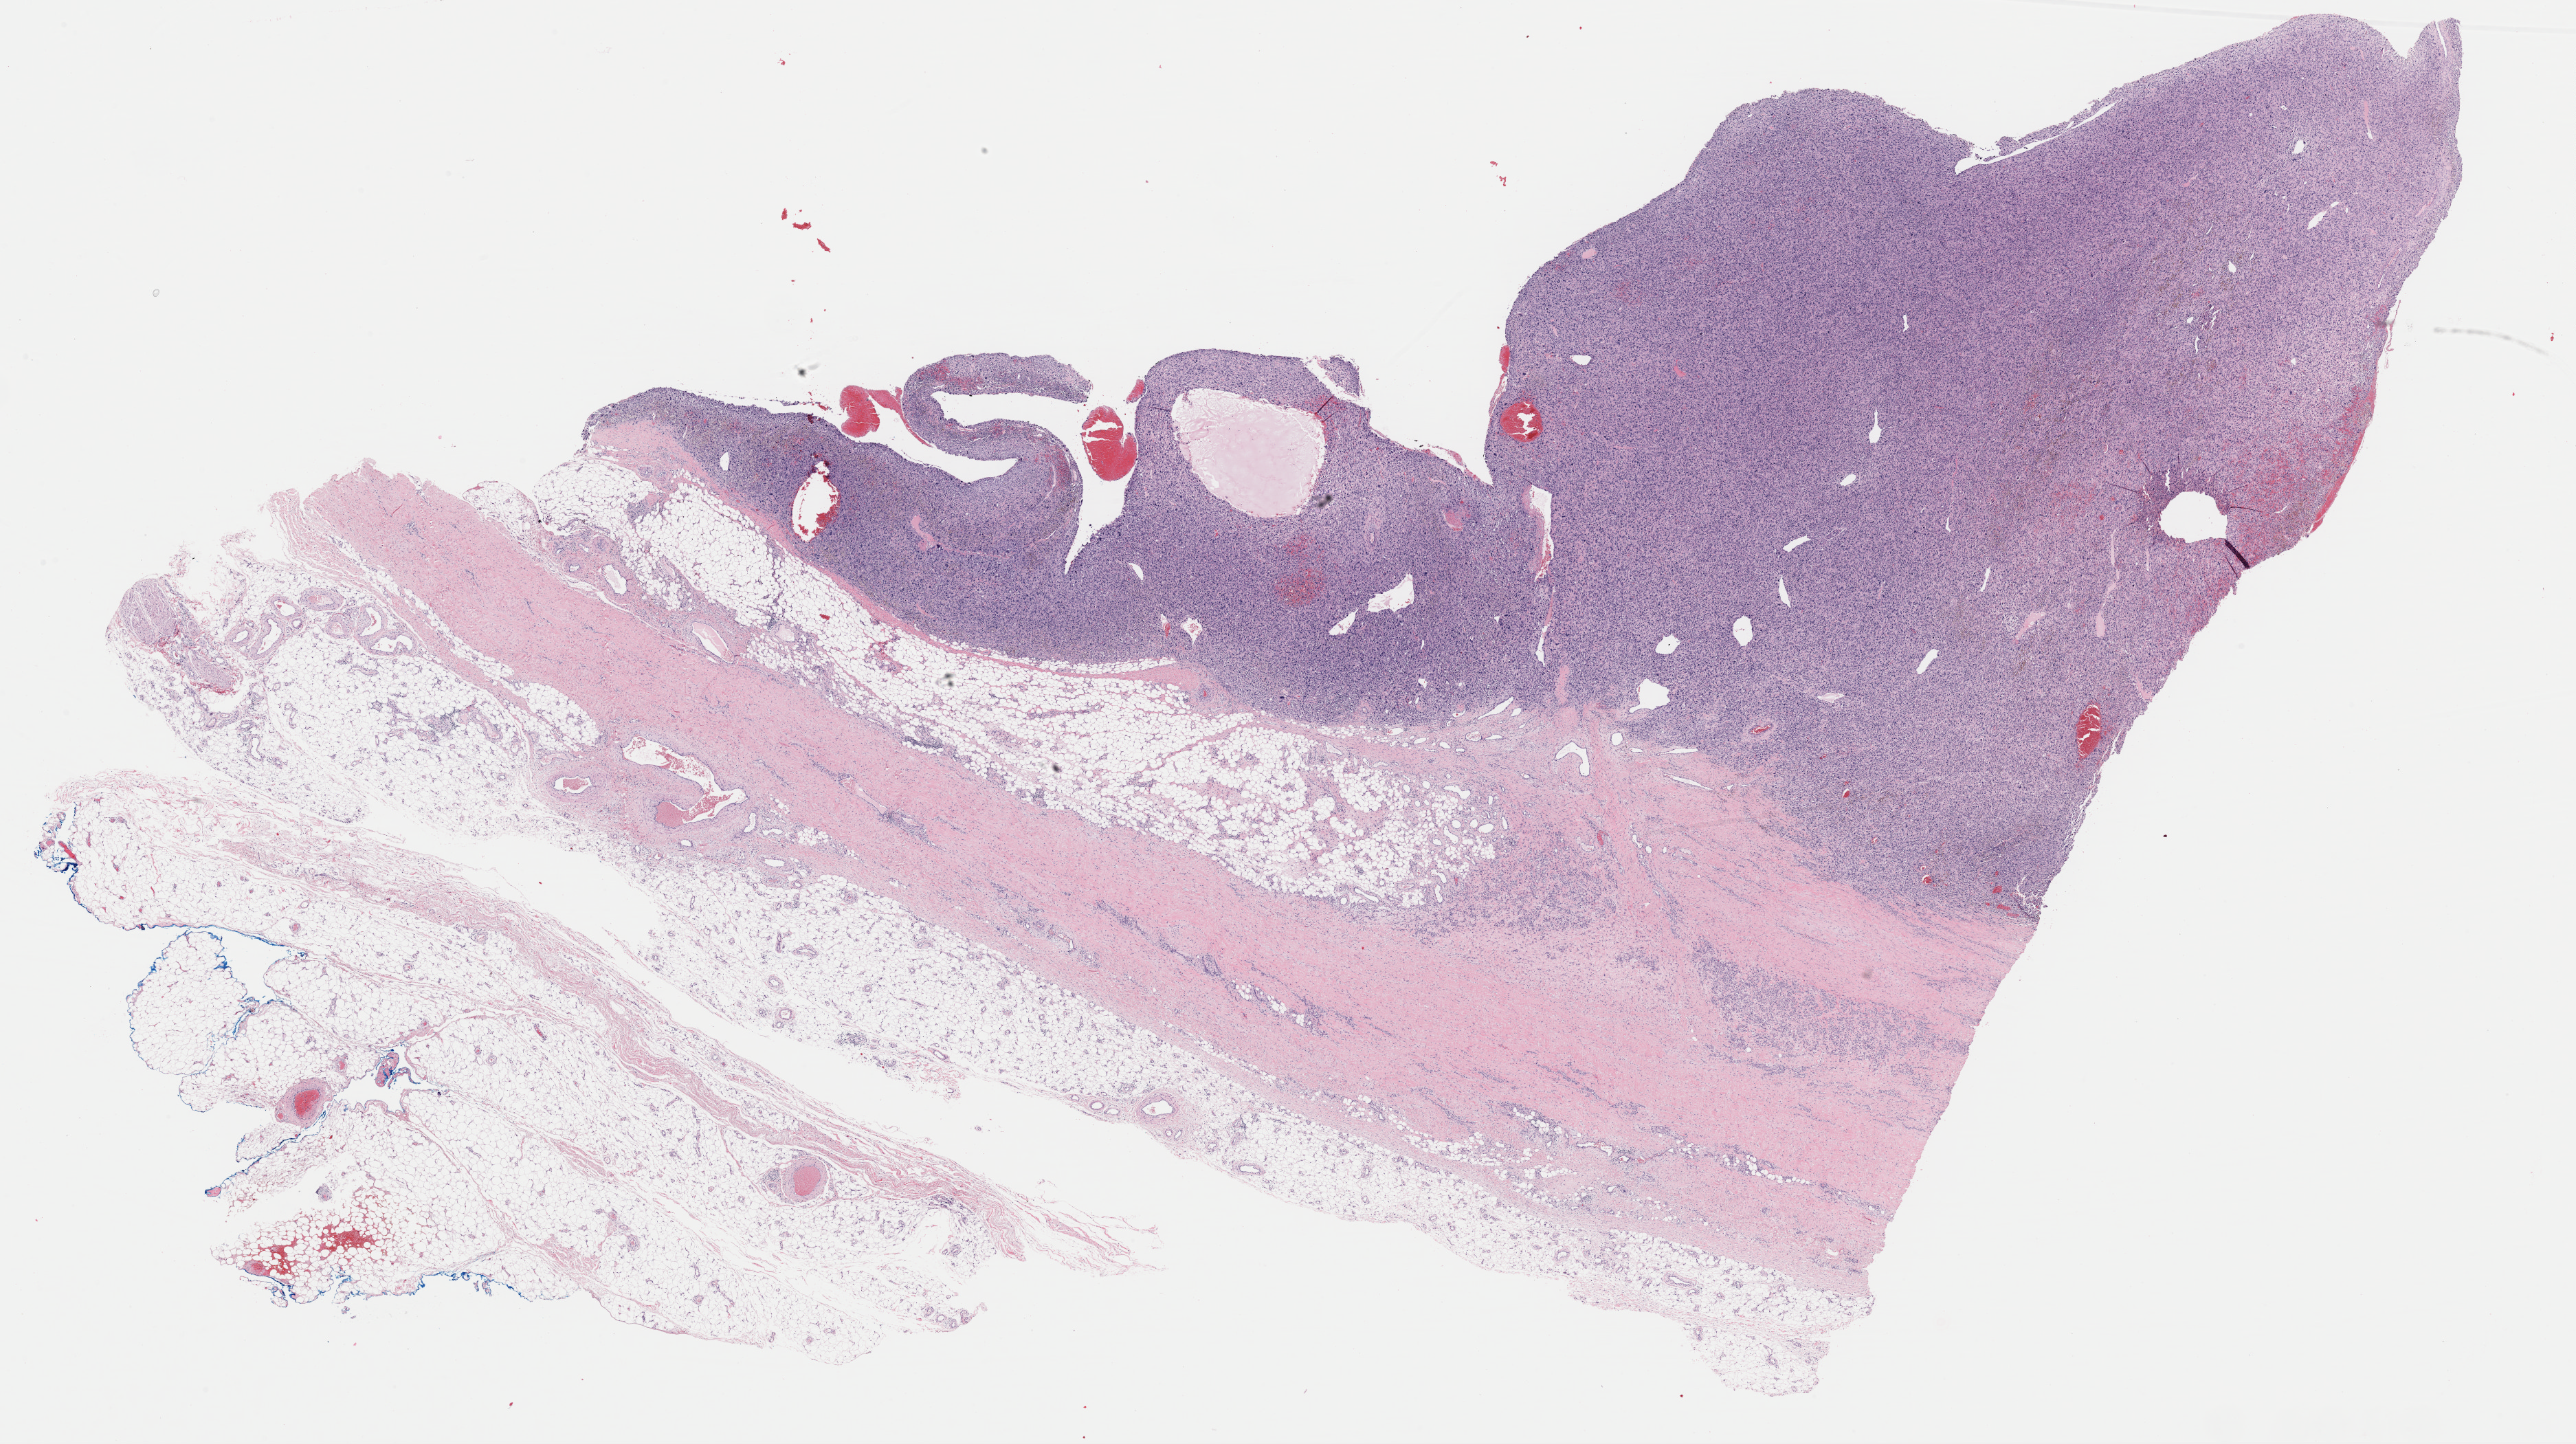
Whole-slide histology image, Hematoxylin and eosin (H&E) stained — whole scanned area (about 29.6 x 16.6 mm, from a 40x scan) shown as a low-resolution overview, FFPE section, primary tumour sample from the connective, subcutaneous and other soft tissues. Patient: female, age at initial diagnosis 75 years.
Diagnosis: Malignant fibrous histiocytoma (connective, subcutaneous and other soft tissues of lower limb and hip).